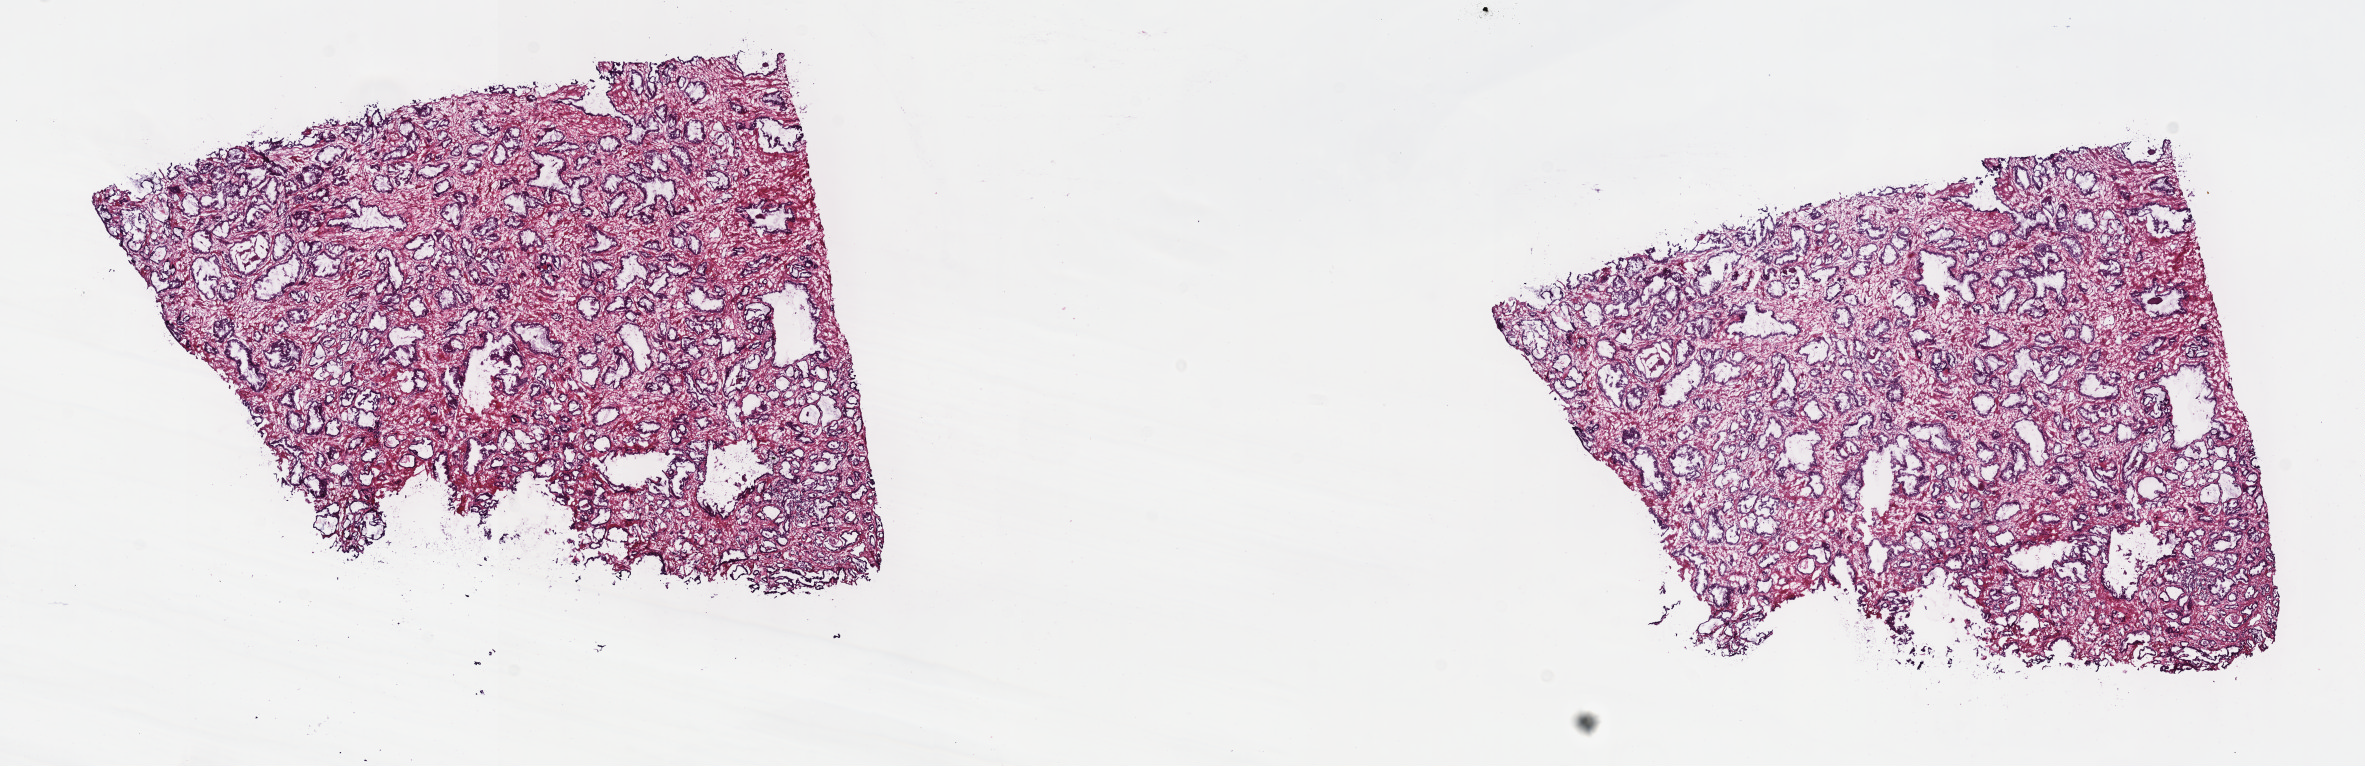
Digitized Hematoxylin and eosin (H&E) stained tissue section (whole slide), a low-resolution overview of the entire scanned area, about 19.1 x 6.2 mm (slide scanned at 40x); frozen section from the top of the tissue portion; primary tumour sample from the prostate. Patient: male, age at initial diagnosis 51 years.
Histologic diagnosis: Infiltrating duct carcinoma, NOS (prostate gland).